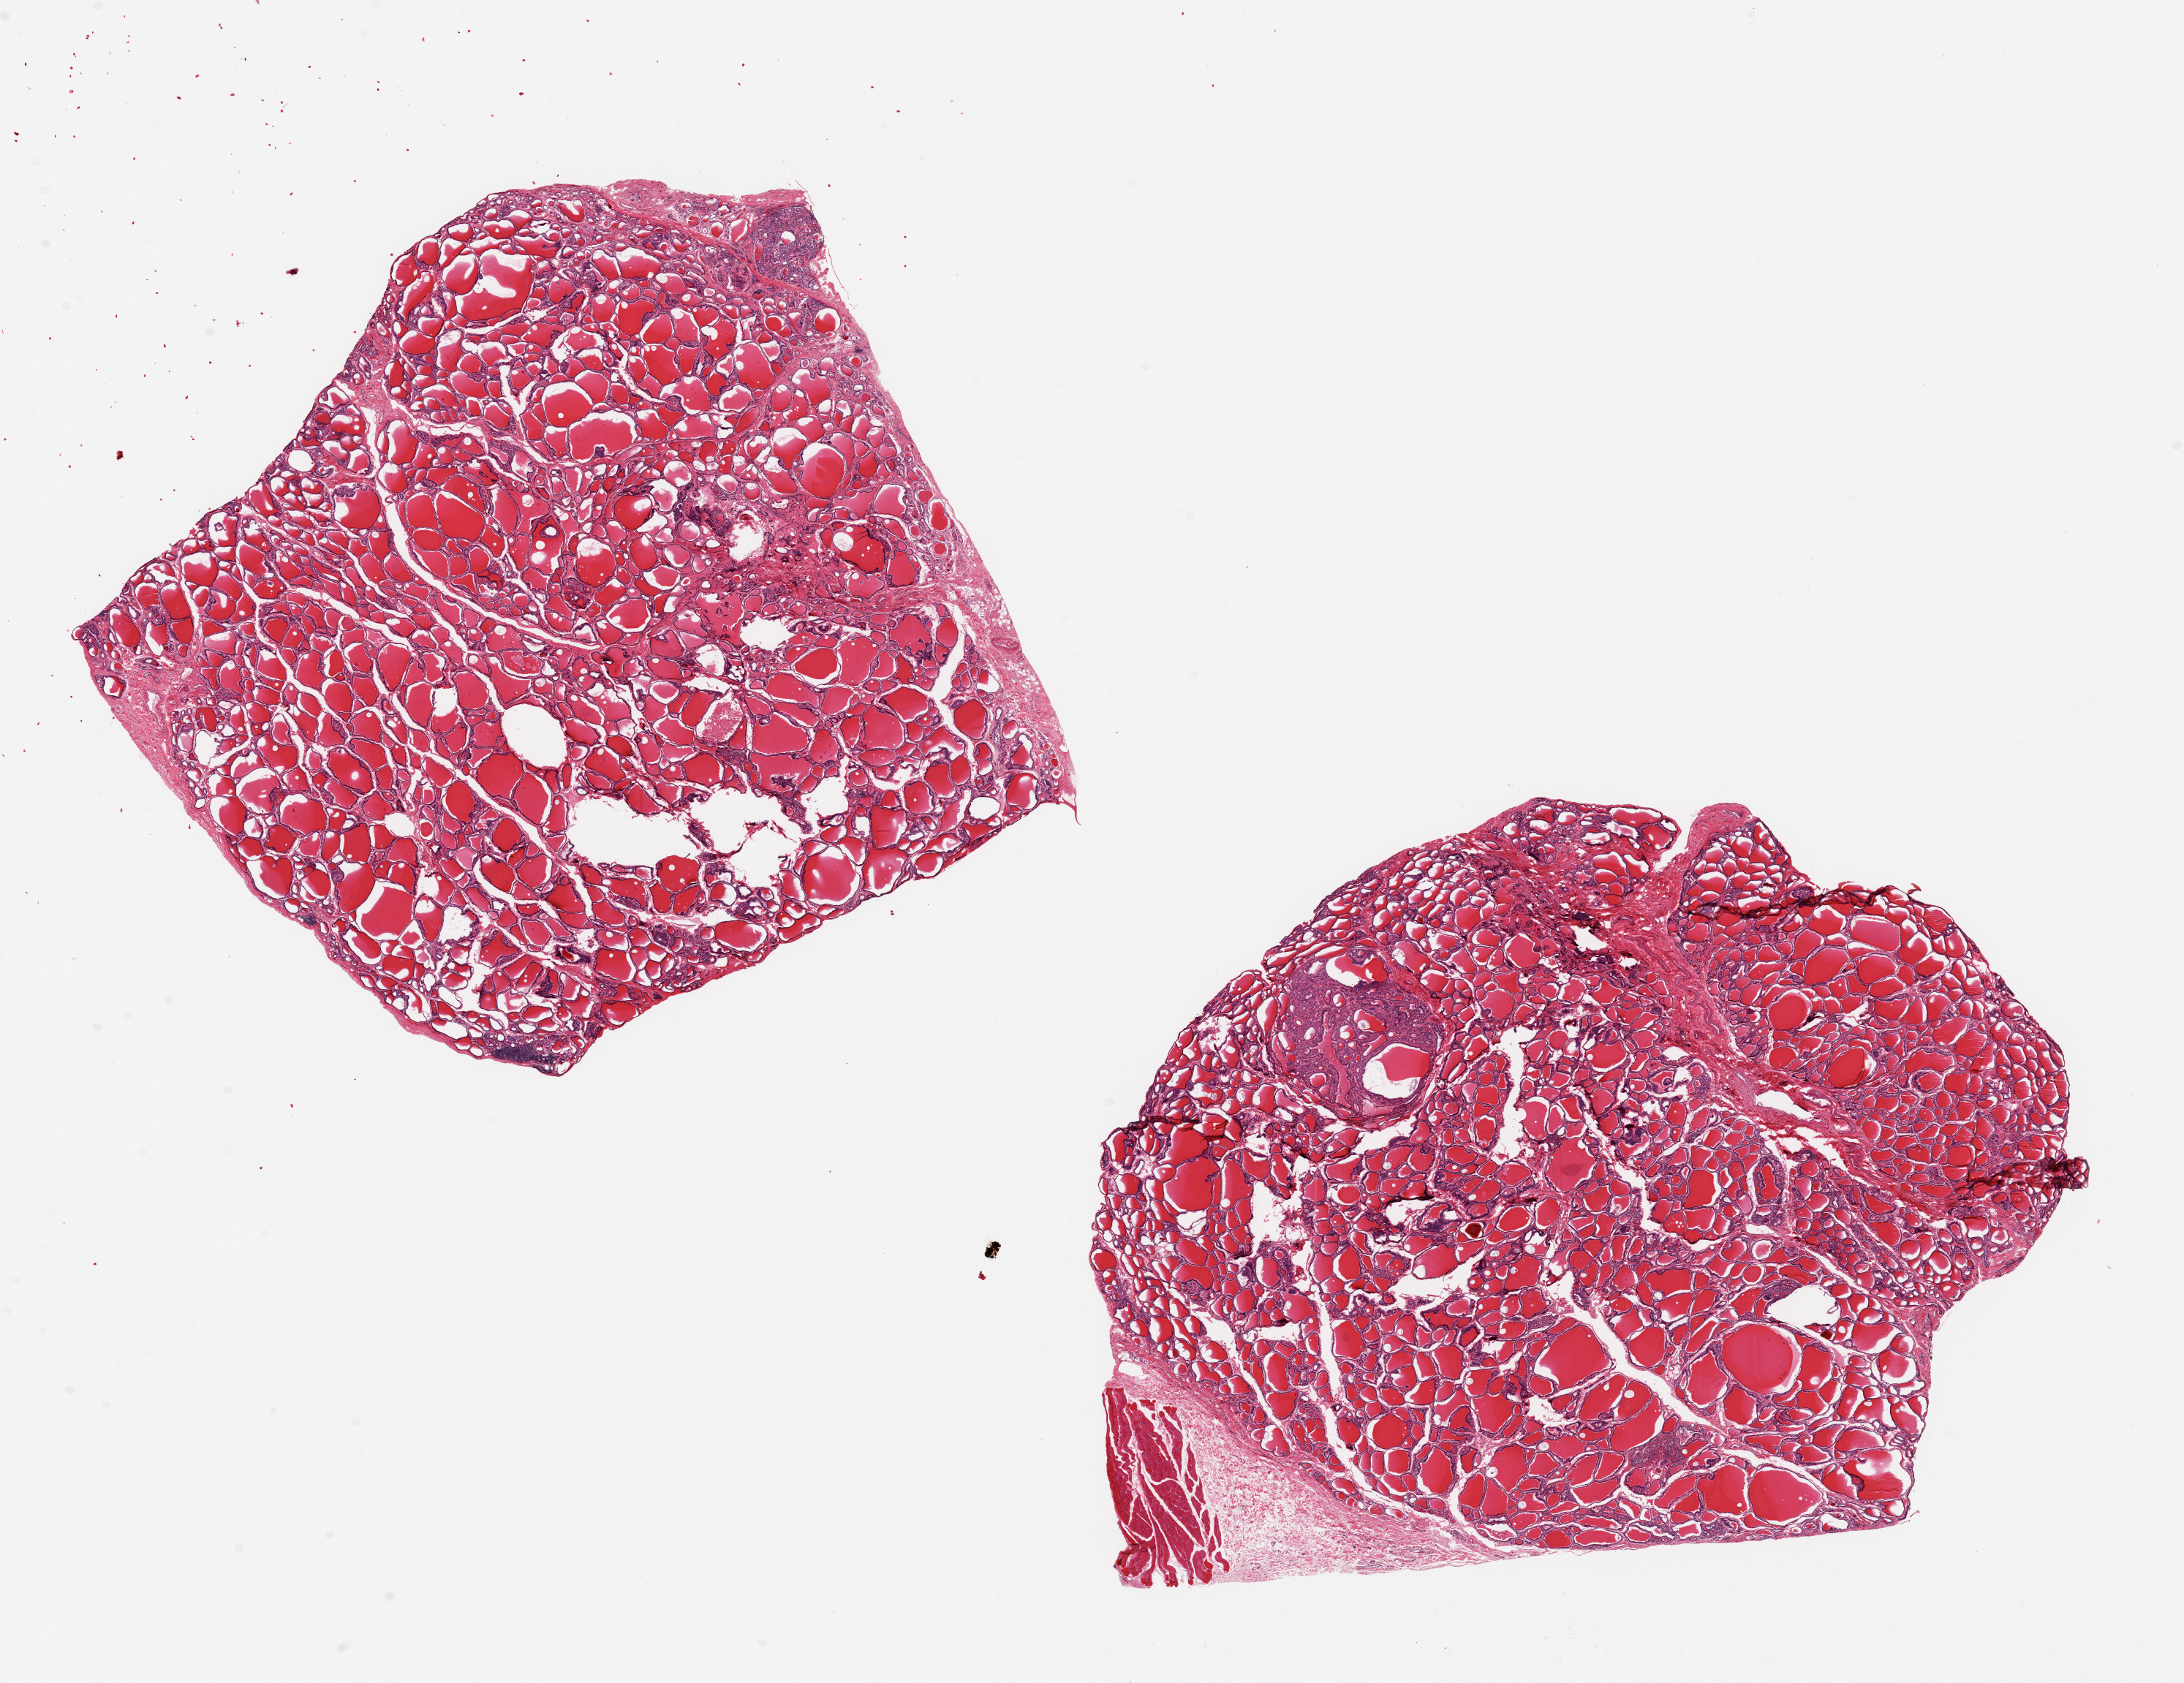
Whole-slide image, H&E stain, brightfield — shown as a low-resolution overview of the whole scanned area (about 23.6 x 18.2 mm). Female donor.
Specimen: PAXgene-fixed paraffin-embedded (PFPE) section; target tissue: thyroid; tissue donor sample.